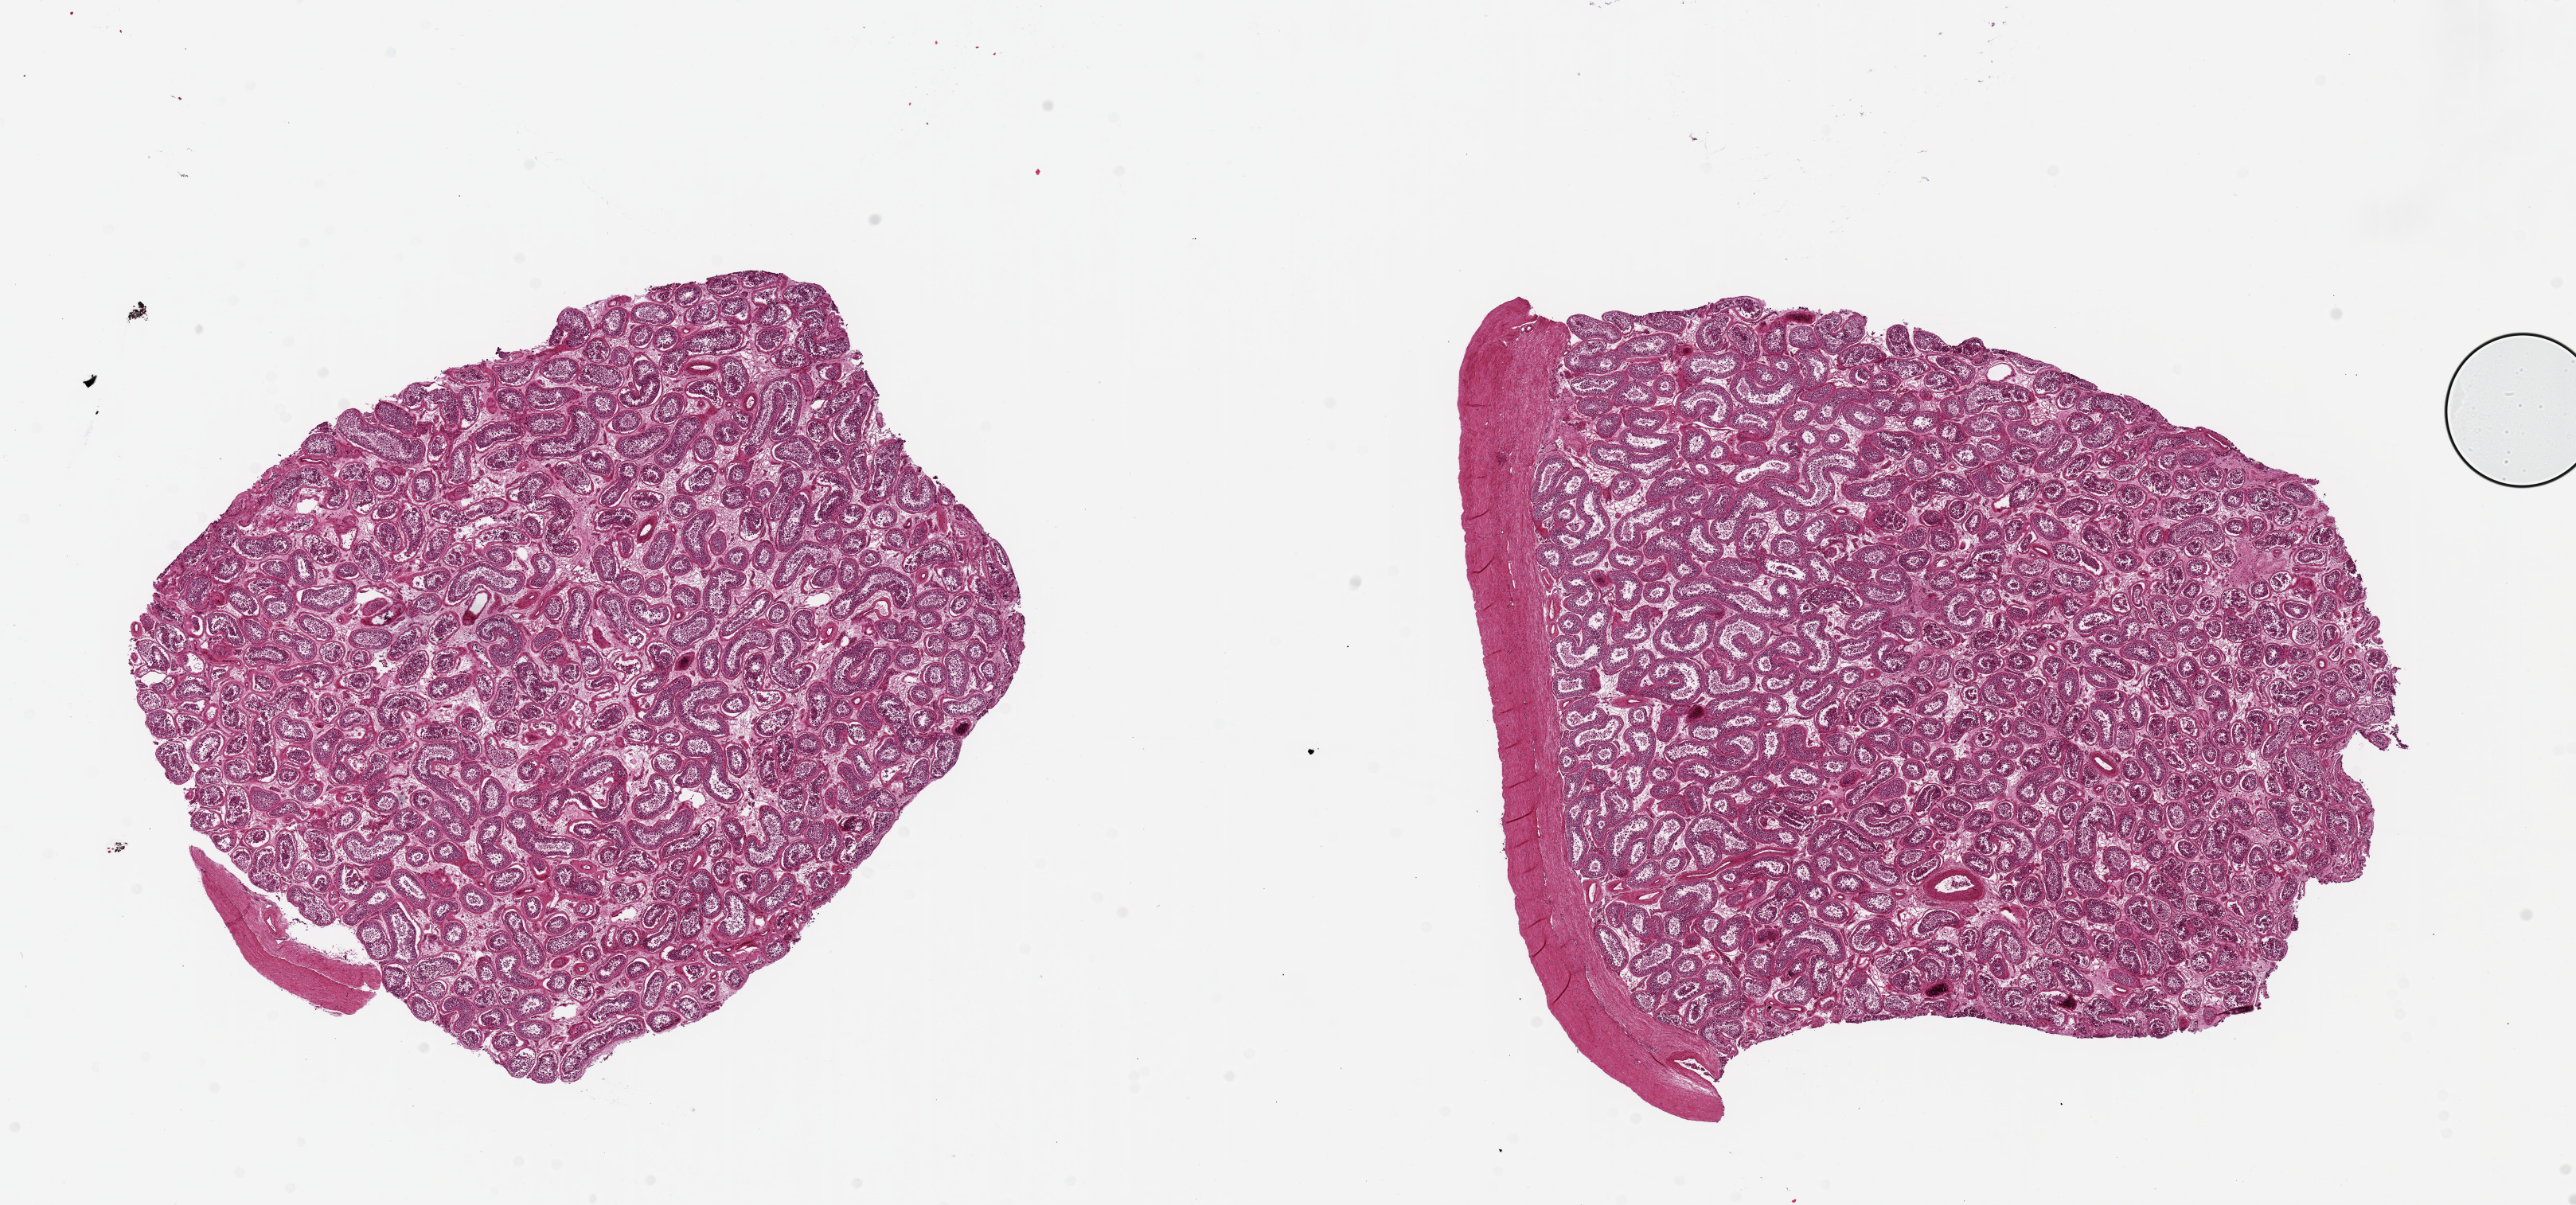
H&E whole-slide image, brightfield, shown as a low-resolution overview of the whole scanned area (about 25.6 x 12.0 mm); PAXgene-fixed paraffin-embedded (PFPE) section; sampled site (target tissue): testis; donor tissue sample. Donor: male.
Review note (as recorded): 2 pieces, 8.5x7 & 9x8mm; spermatogenesis present, not well preserved.